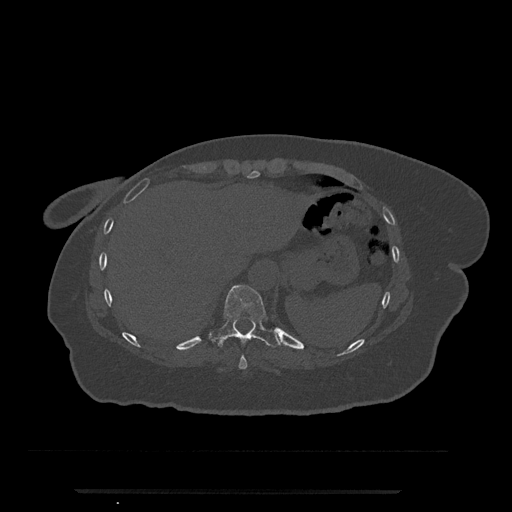
CT including the spine, one axial slice; position 297 of 797 along the scan axis; reconstruction kernel Br40s/3; bone window (W 1800 / L 400 HU); 0.5 mm slice thickness; 512 × 512 image matrix, field of view 440 × 440 mm. Female patient, age 51 years. From the clinical record (not read from this slice): primary cancer: neuro; vertebrae with lytic lesions (as recorded): T8.
Annotated regions visible in this slice (semi-automatically segmented with operator editing):
- T10 vertebra: box from (x=211, y=285) to (x=279, y=348) px
- T9 vertebra: (x=238, y=355)–(x=247, y=370)